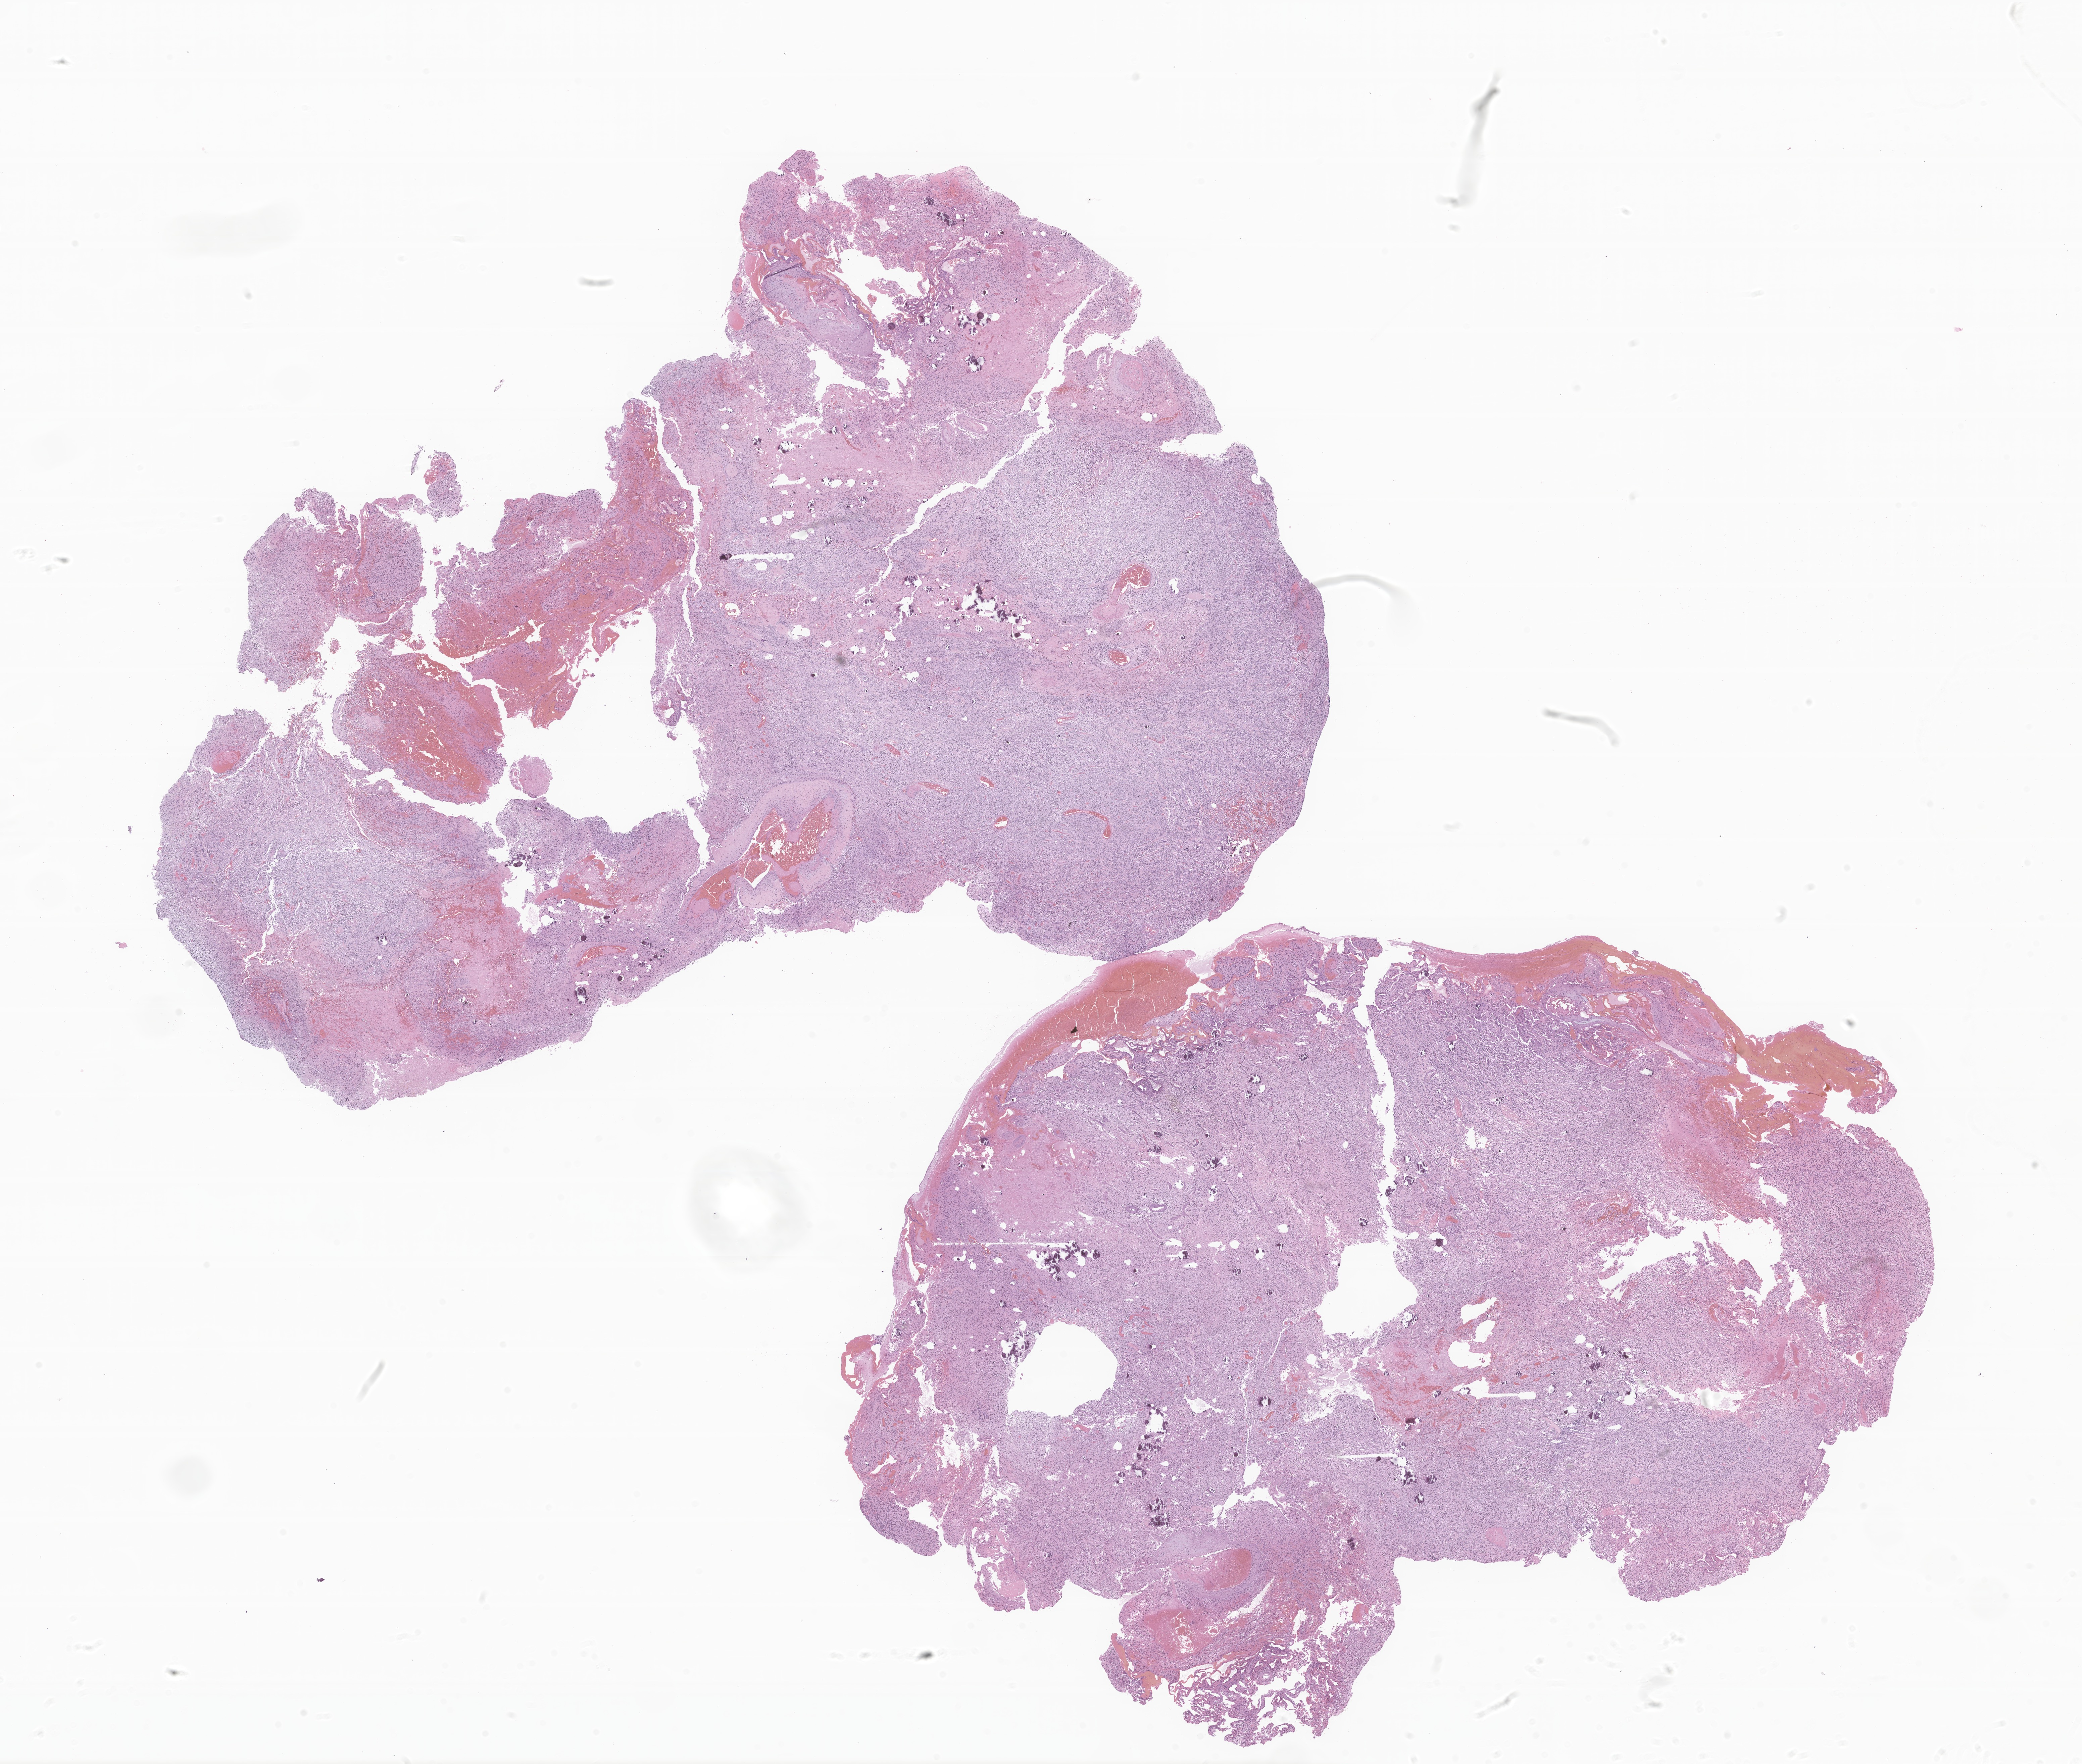
Whole-slide image, haematoxylin and eosin stain of tumor tissue from the brain — whole scanned area (about 26.2 x 22.2 mm) shown as a low-resolution overview. Formalin-fixed, paraffin-embedded (FFPE) tissue. Patient: female, age 178 months (14 years 10 months).
Diagnosis (ICD-O-3 morphology term): Glioma, malignant.